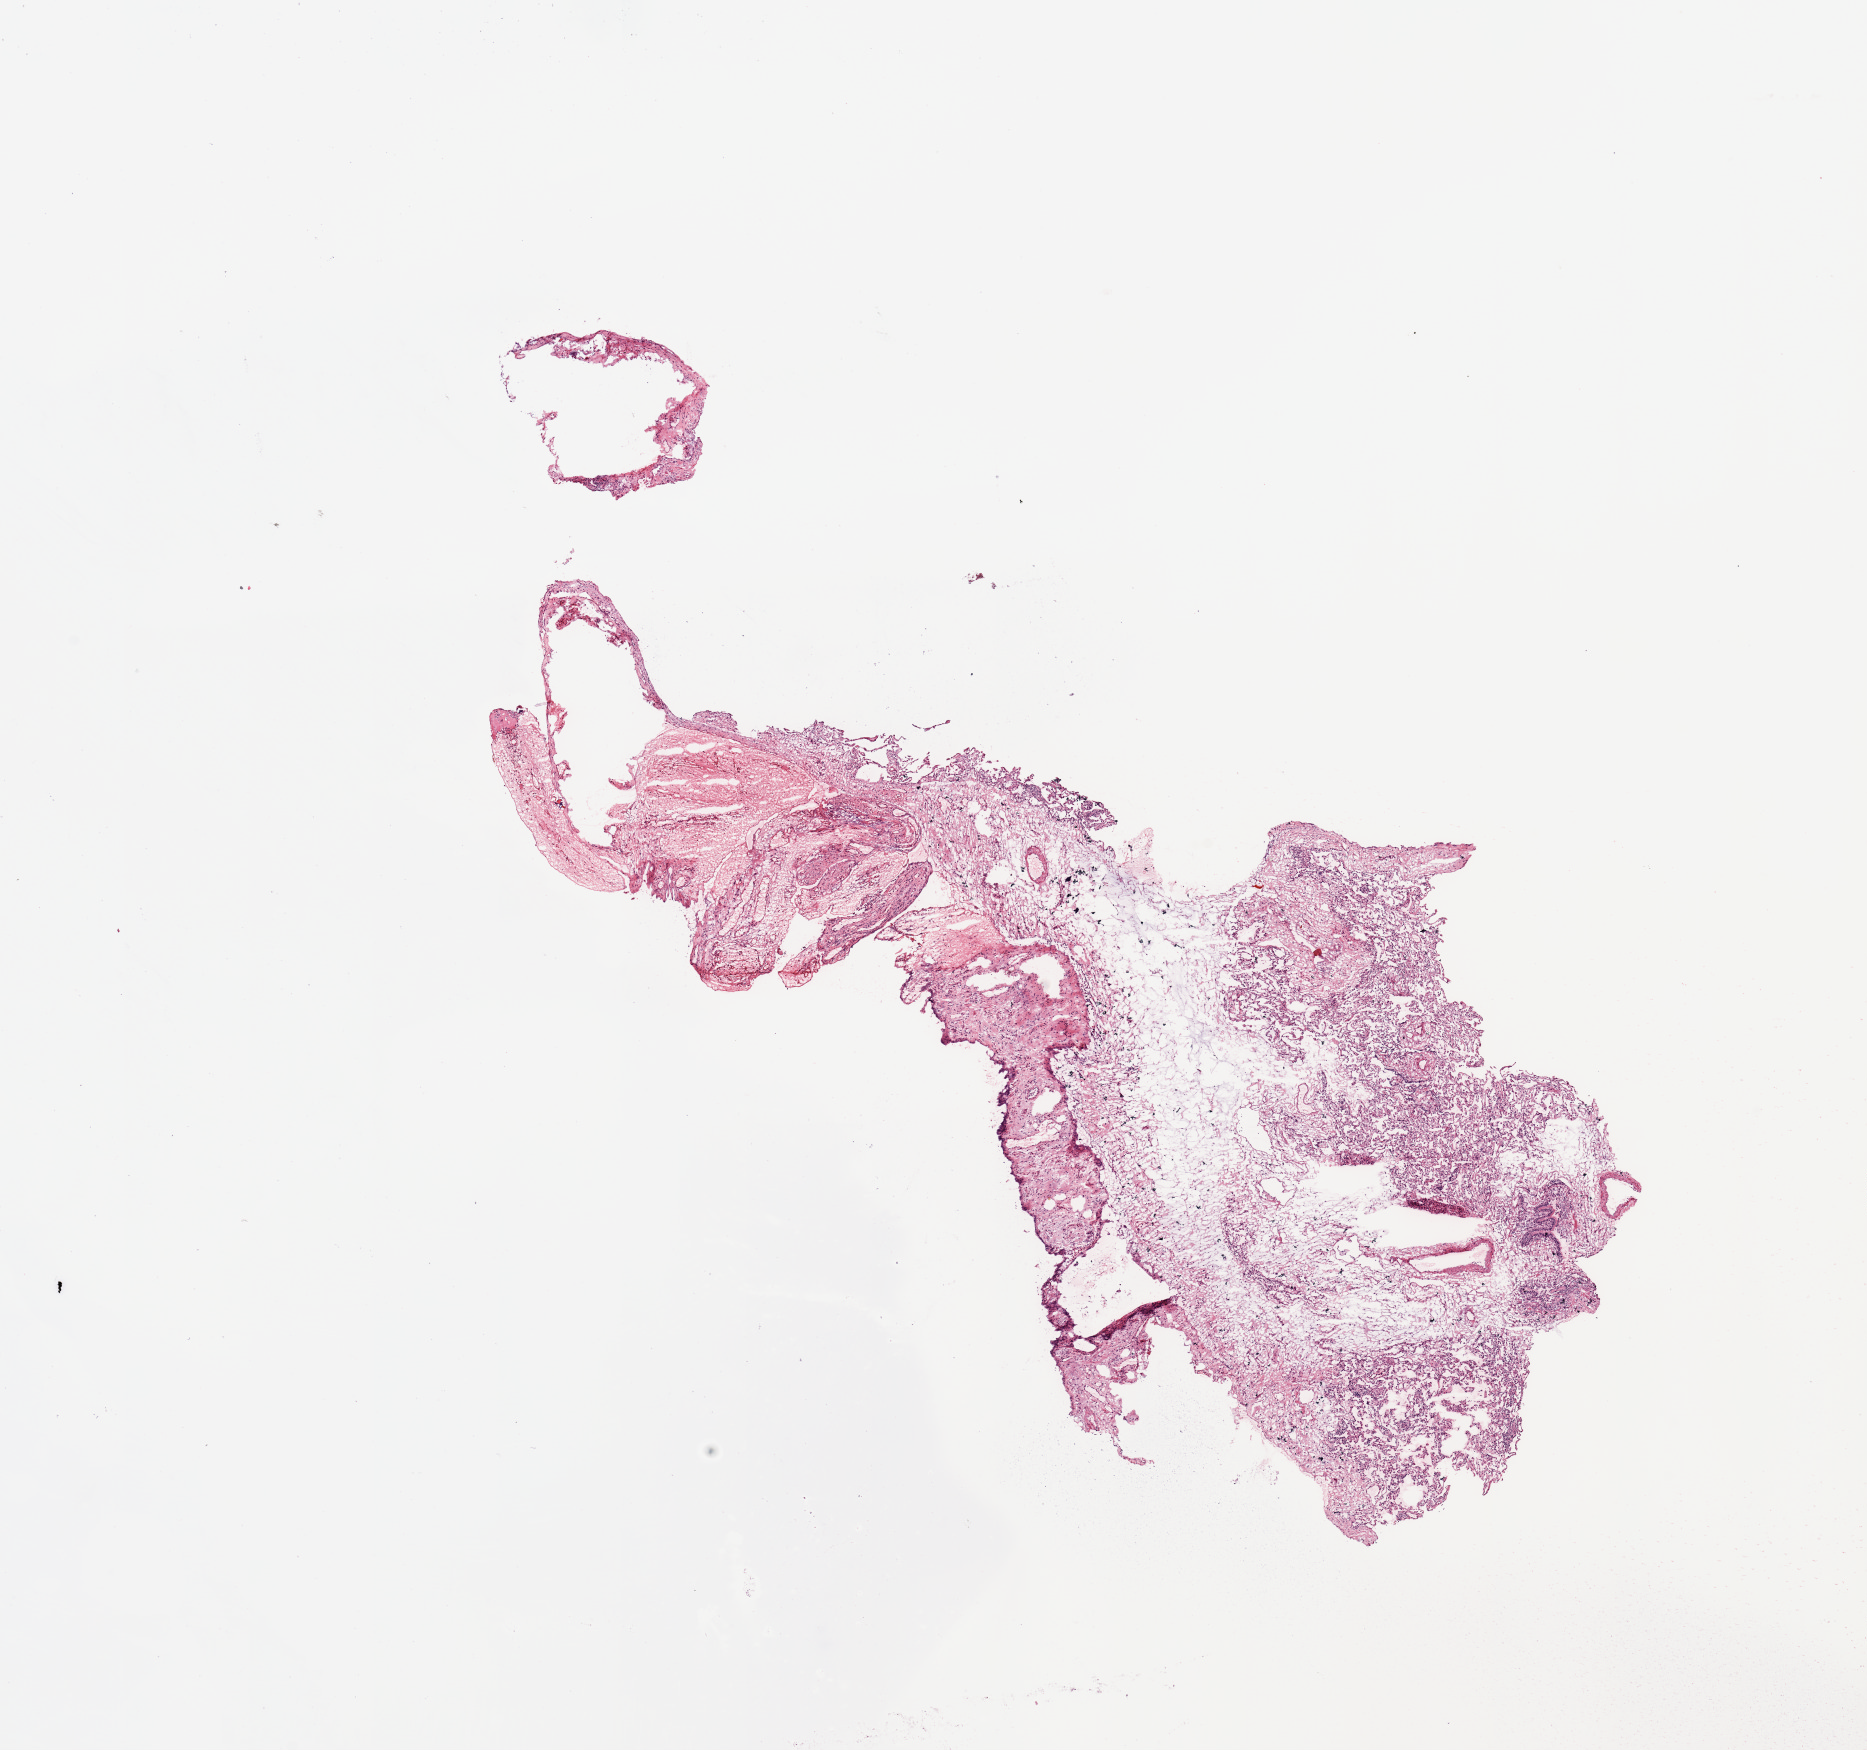
Hematoxylin and eosin (H&E) stained whole-slide image — shown as a low-resolution overview of the whole scanned area (about 14.8 x 13.8 mm, acquisition: 20x scan); normal (non-tumour) tissue sample, lung. Male, 79 y/o.
This section: normal (non-tumour) tissue from the same patient. Patient diagnosis: Adenocarcinoma, NOS.